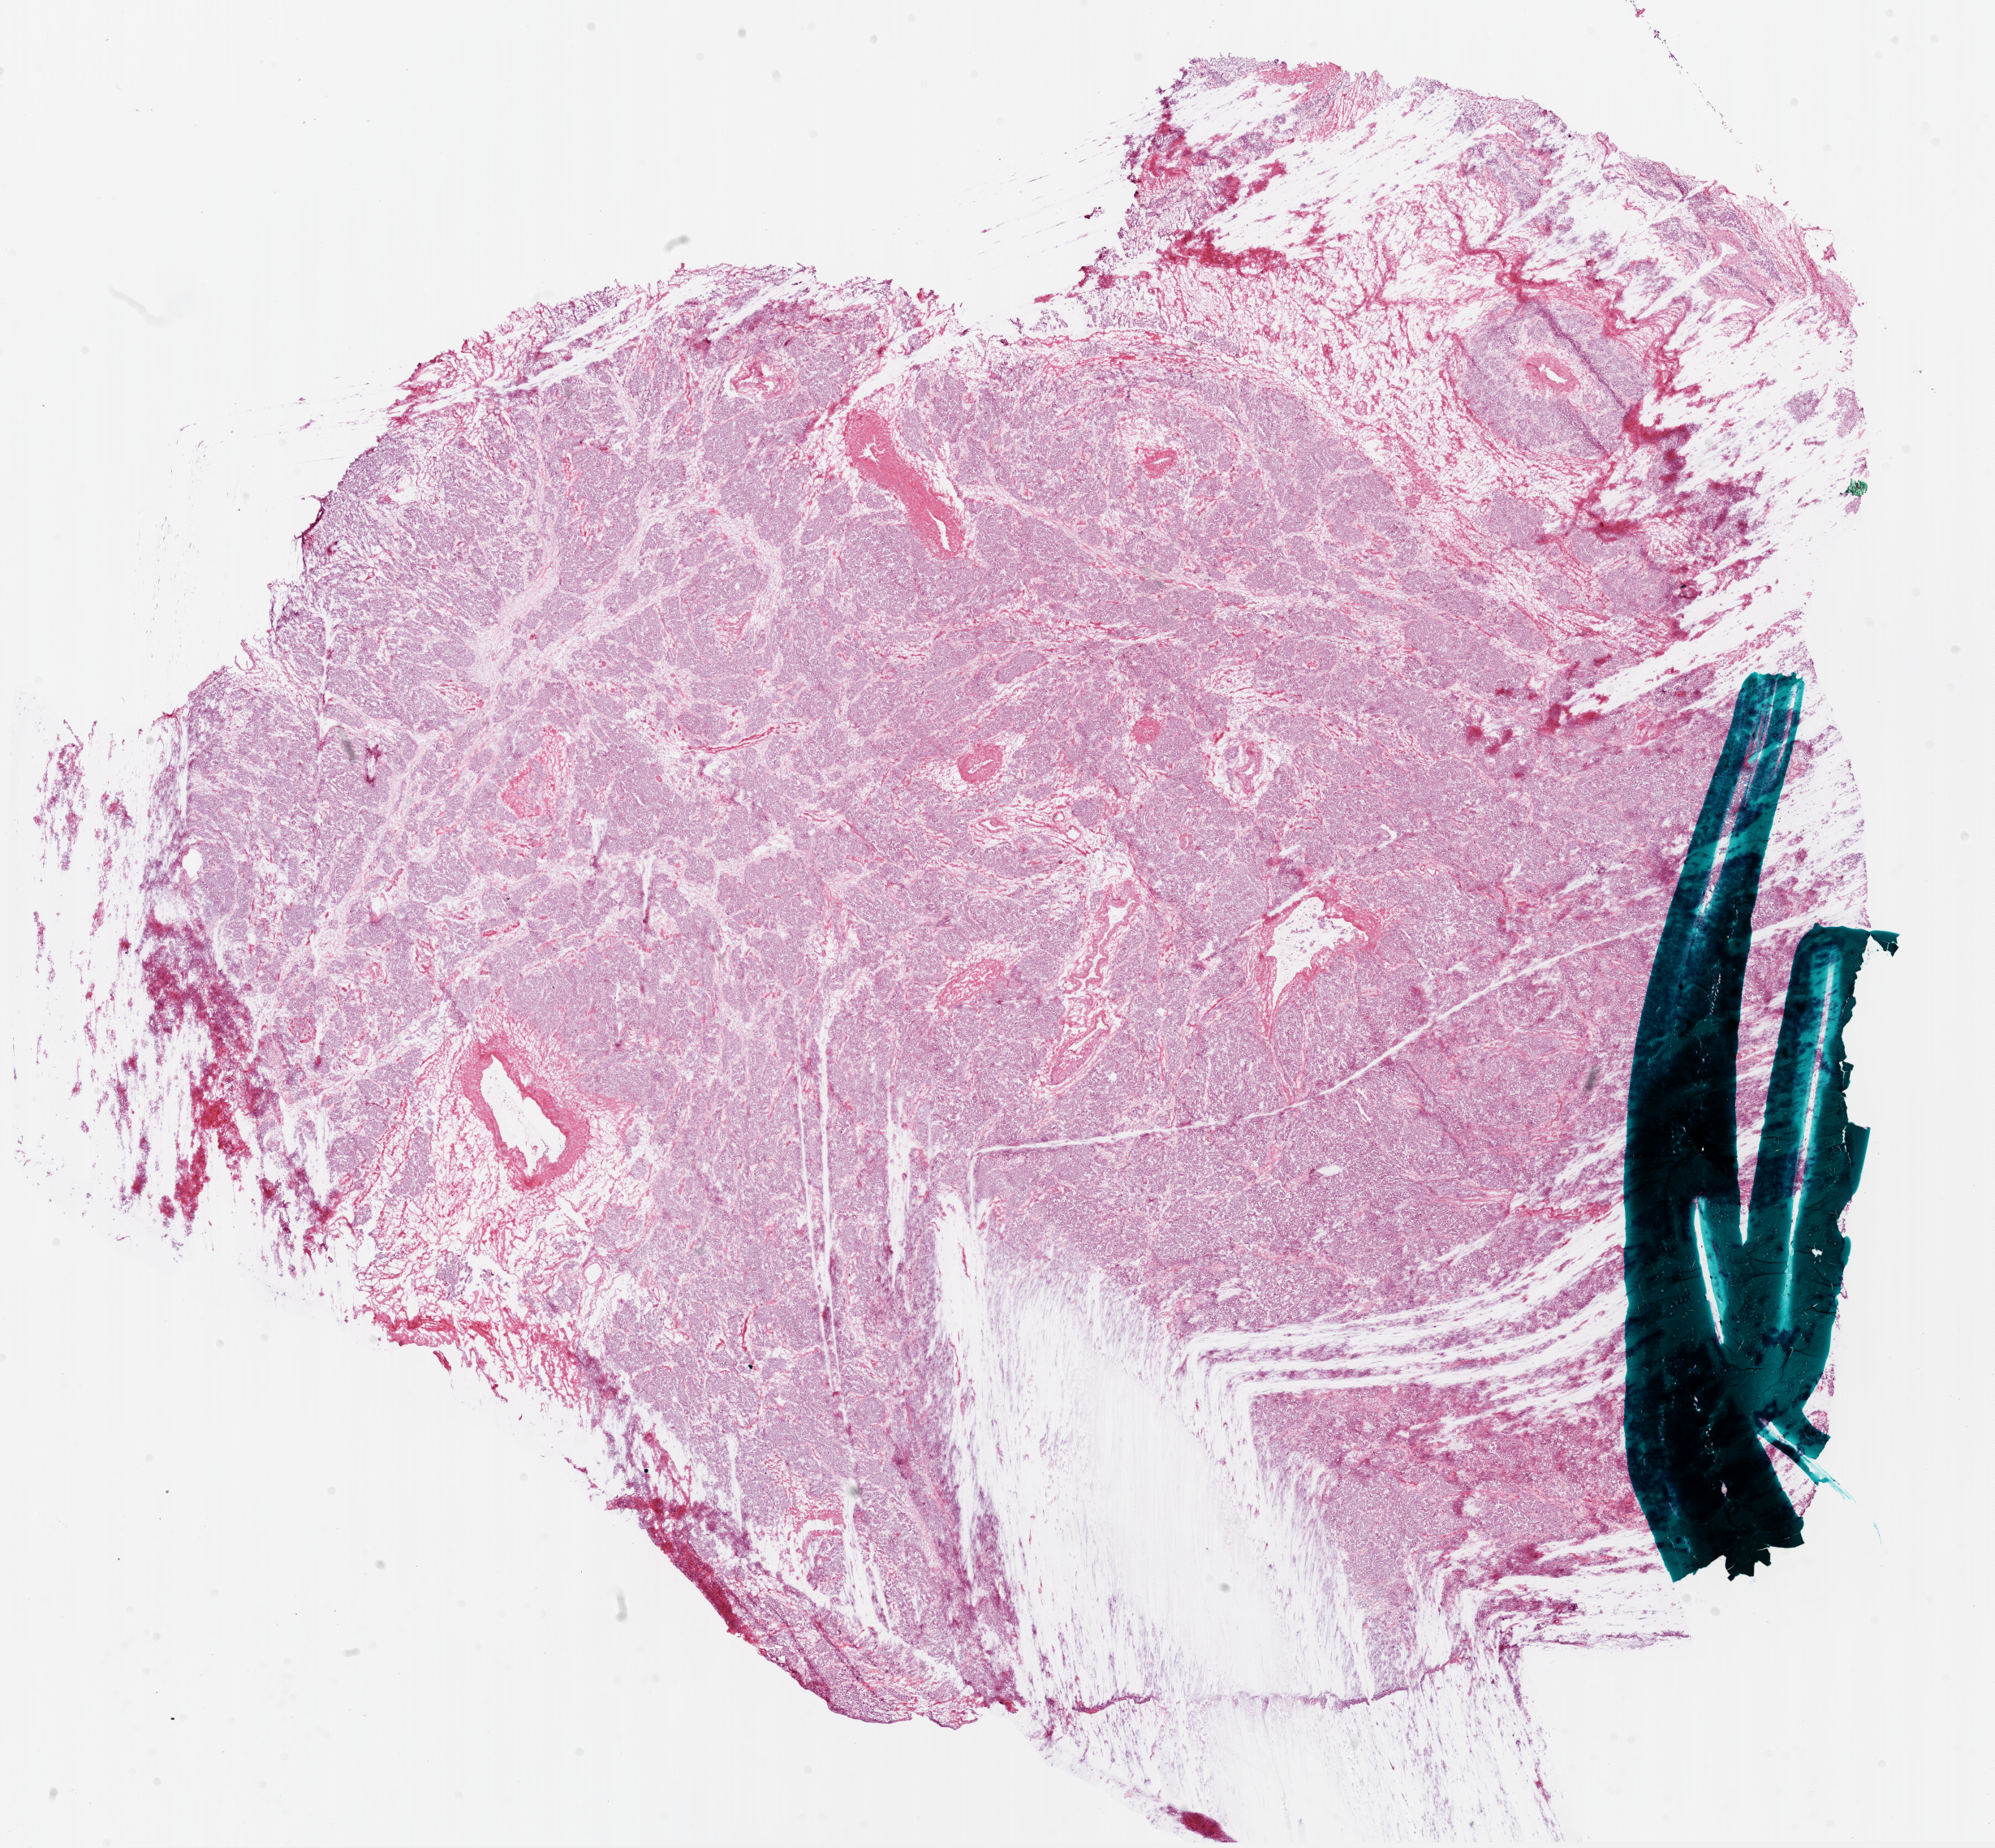
Digitized H&E tissue section (whole slide) — low-resolution overview of the scanned area, about 19.8 x 18.4 mm (acquisition: 20x scan). Frozen section from the bottom of the tissue portion. Primary tumour sample from the ovary. Female patient; age at initial diagnosis 77 years. Histologic grade: G3 (poorly differentiated). Slide review estimates, as recorded: tumour cells 95%, tumour nuclei 97%, stromal cells 5%, necrosis 5%.
* FIGO stage: IV
* pathologic diagnosis: Serous cystadenocarcinoma, NOS